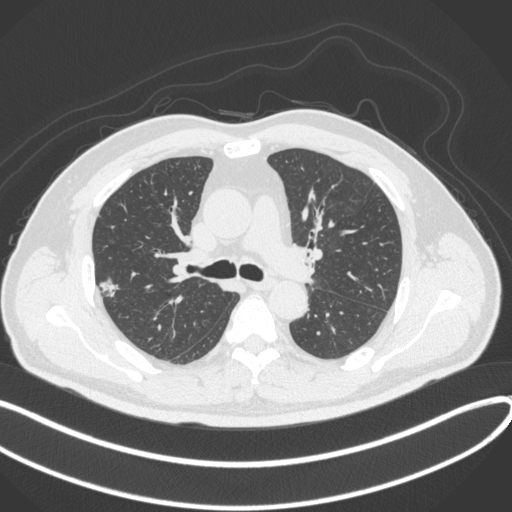
Chest CT, one axial slice. Position 219 of 373 along the scan axis. Reconstruction kernel B31f. 120 kVp. Lung window (W 1500 / L -600 HU). 1 mm slice thickness. 512 × 512 image matrix, field of view 400 × 400 mm. Patient: male, 60 years. From the clinical record (not read from this slice): clinical TNM (as recorded): T1c N0 M0.
Outlined on this slice (bounding box drawn by a radiologist):
- lung tumour (recorded histology: adenocarcinoma): bounding box [x1, y1, x2, y2] px = [95, 272, 123, 300]